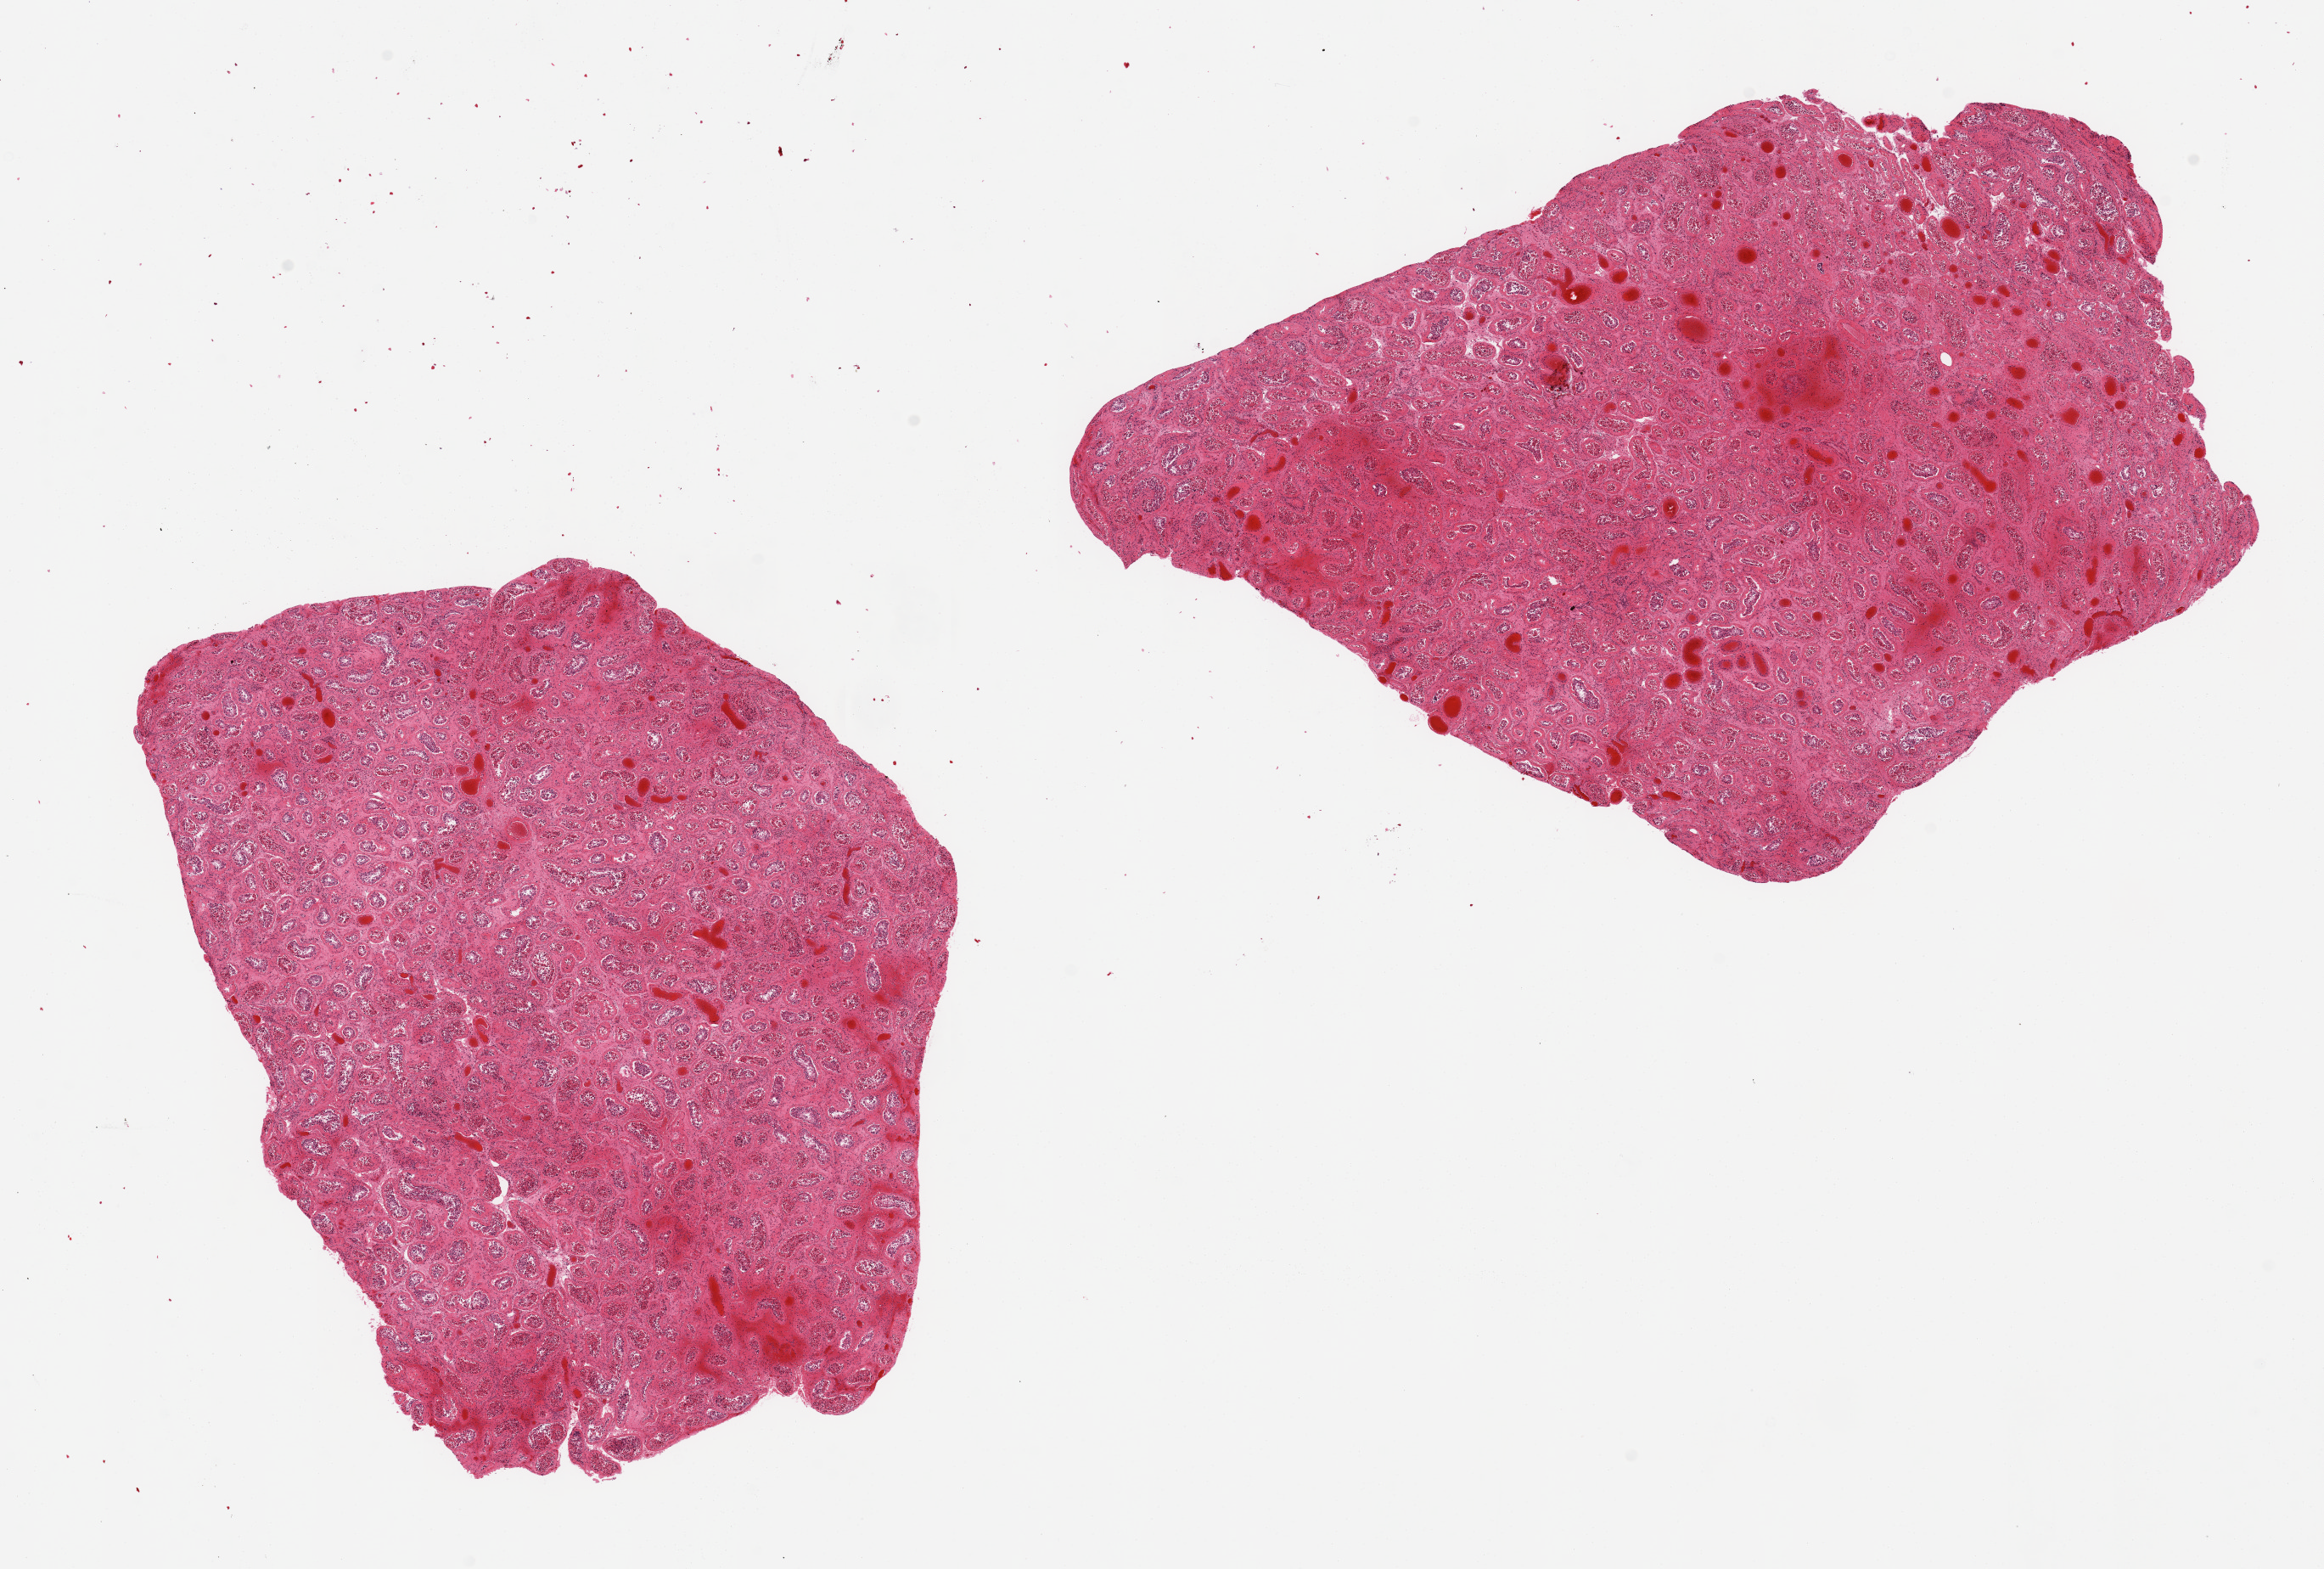
Digitized H&E-stained section — shown as a low-resolution overview of the whole scanned area (about 21.7 x 14.6 mm, acquisition: 20x scan); PAXgene-fixed paraffin-embedded (PFPE) section; sampled site (target tissue): testis; donor tissue sample. Male donor.
Reviewer comment on this tissue sample: 2 pieces, spermatogenesis is present; moderately autolyzed.